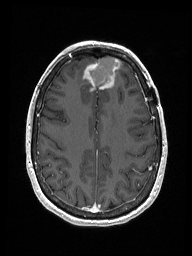
Brain MRI from a brain-tumour surgery series, one axial slice. Slice 56 of 192 in the series (ordered by position). T1-weighted post-contrast. 1 mm slice thickness. 192 × 256 image matrix, field of view 187 × 250 mm. Case-level facts recorded for this patient, not image findings: histopathology: Metastastic Carcinoma from Breast primary; tumour location: Right Frontal.
Annotated regions visible in this slice (expert manual segmentation):
- previous resection cavity: box from (x=90, y=57) to (x=118, y=86) px